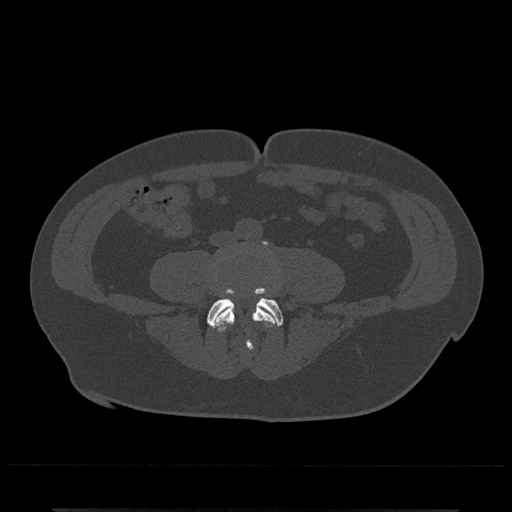
CT including the spine, one axial slice. Reconstruction kernel Br40s/3. Bone window (W 1800 / L 400 HU). 0.5 mm slice thickness. 512 × 512 image matrix, field of view 393 × 393 mm. Male patient, age 67 years. Case-level facts recorded for this patient, not image findings: primary cancer: prostate.
Structures marked on this image (semi-automatically segmented with operator editing):
- L4 vertebra: bounding box (x1, y1, x2, y2) in pixels: (212, 241, 279, 351)
- L5 vertebra: (207, 288, 283, 326)